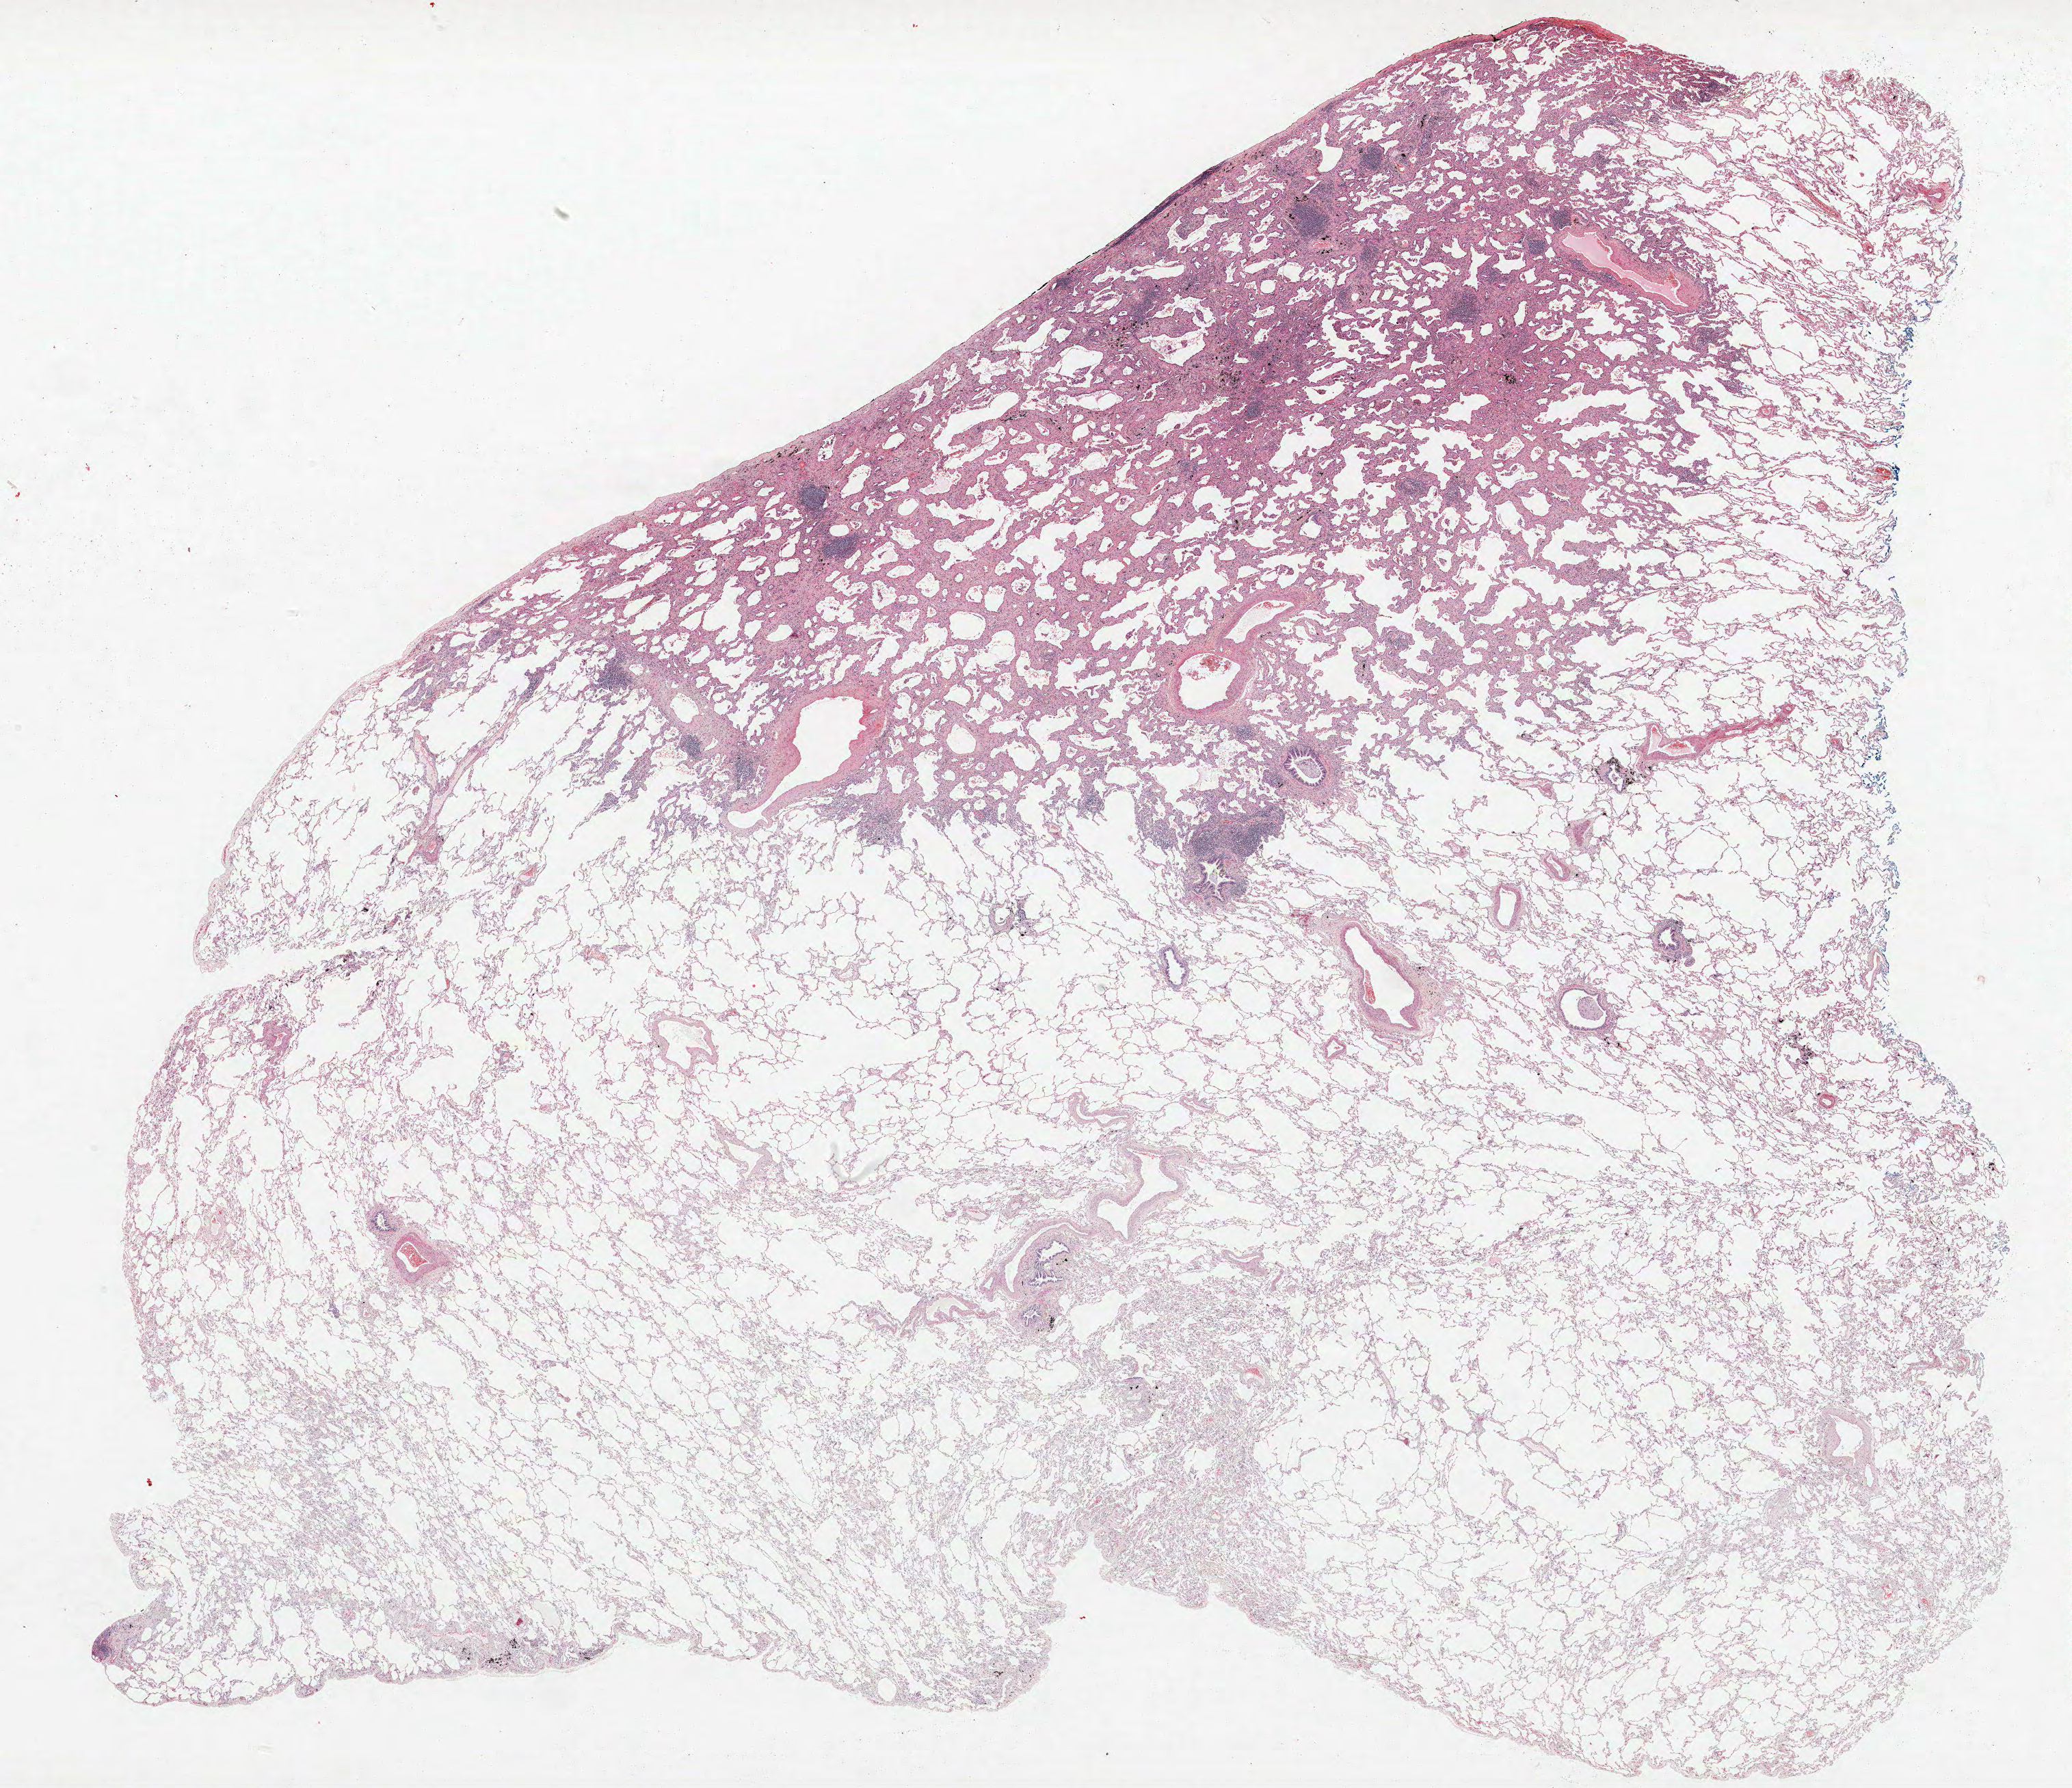
Whole-slide histology image, Hematoxylin and eosin (H&E) stained, shown as a low-resolution overview of the whole scanned area (about 24.2 x 20.9 mm, acquisition: 40x scan), FFPE section, lung. Female, age 68 at enrolment. Former smoker at enrolment. Grade: well differentiated (G1).
Stage (AJCC 6th edition): IA. ICD-O-3 topography: lower lobe of lung (C34.3). Participant's lung-cancer diagnosis: Bronchiolo-alveolar adenocarcinoma, NOS. Tumour size (pathology): 15 mm. Primary tumour location (clinical record): right lower lobe.